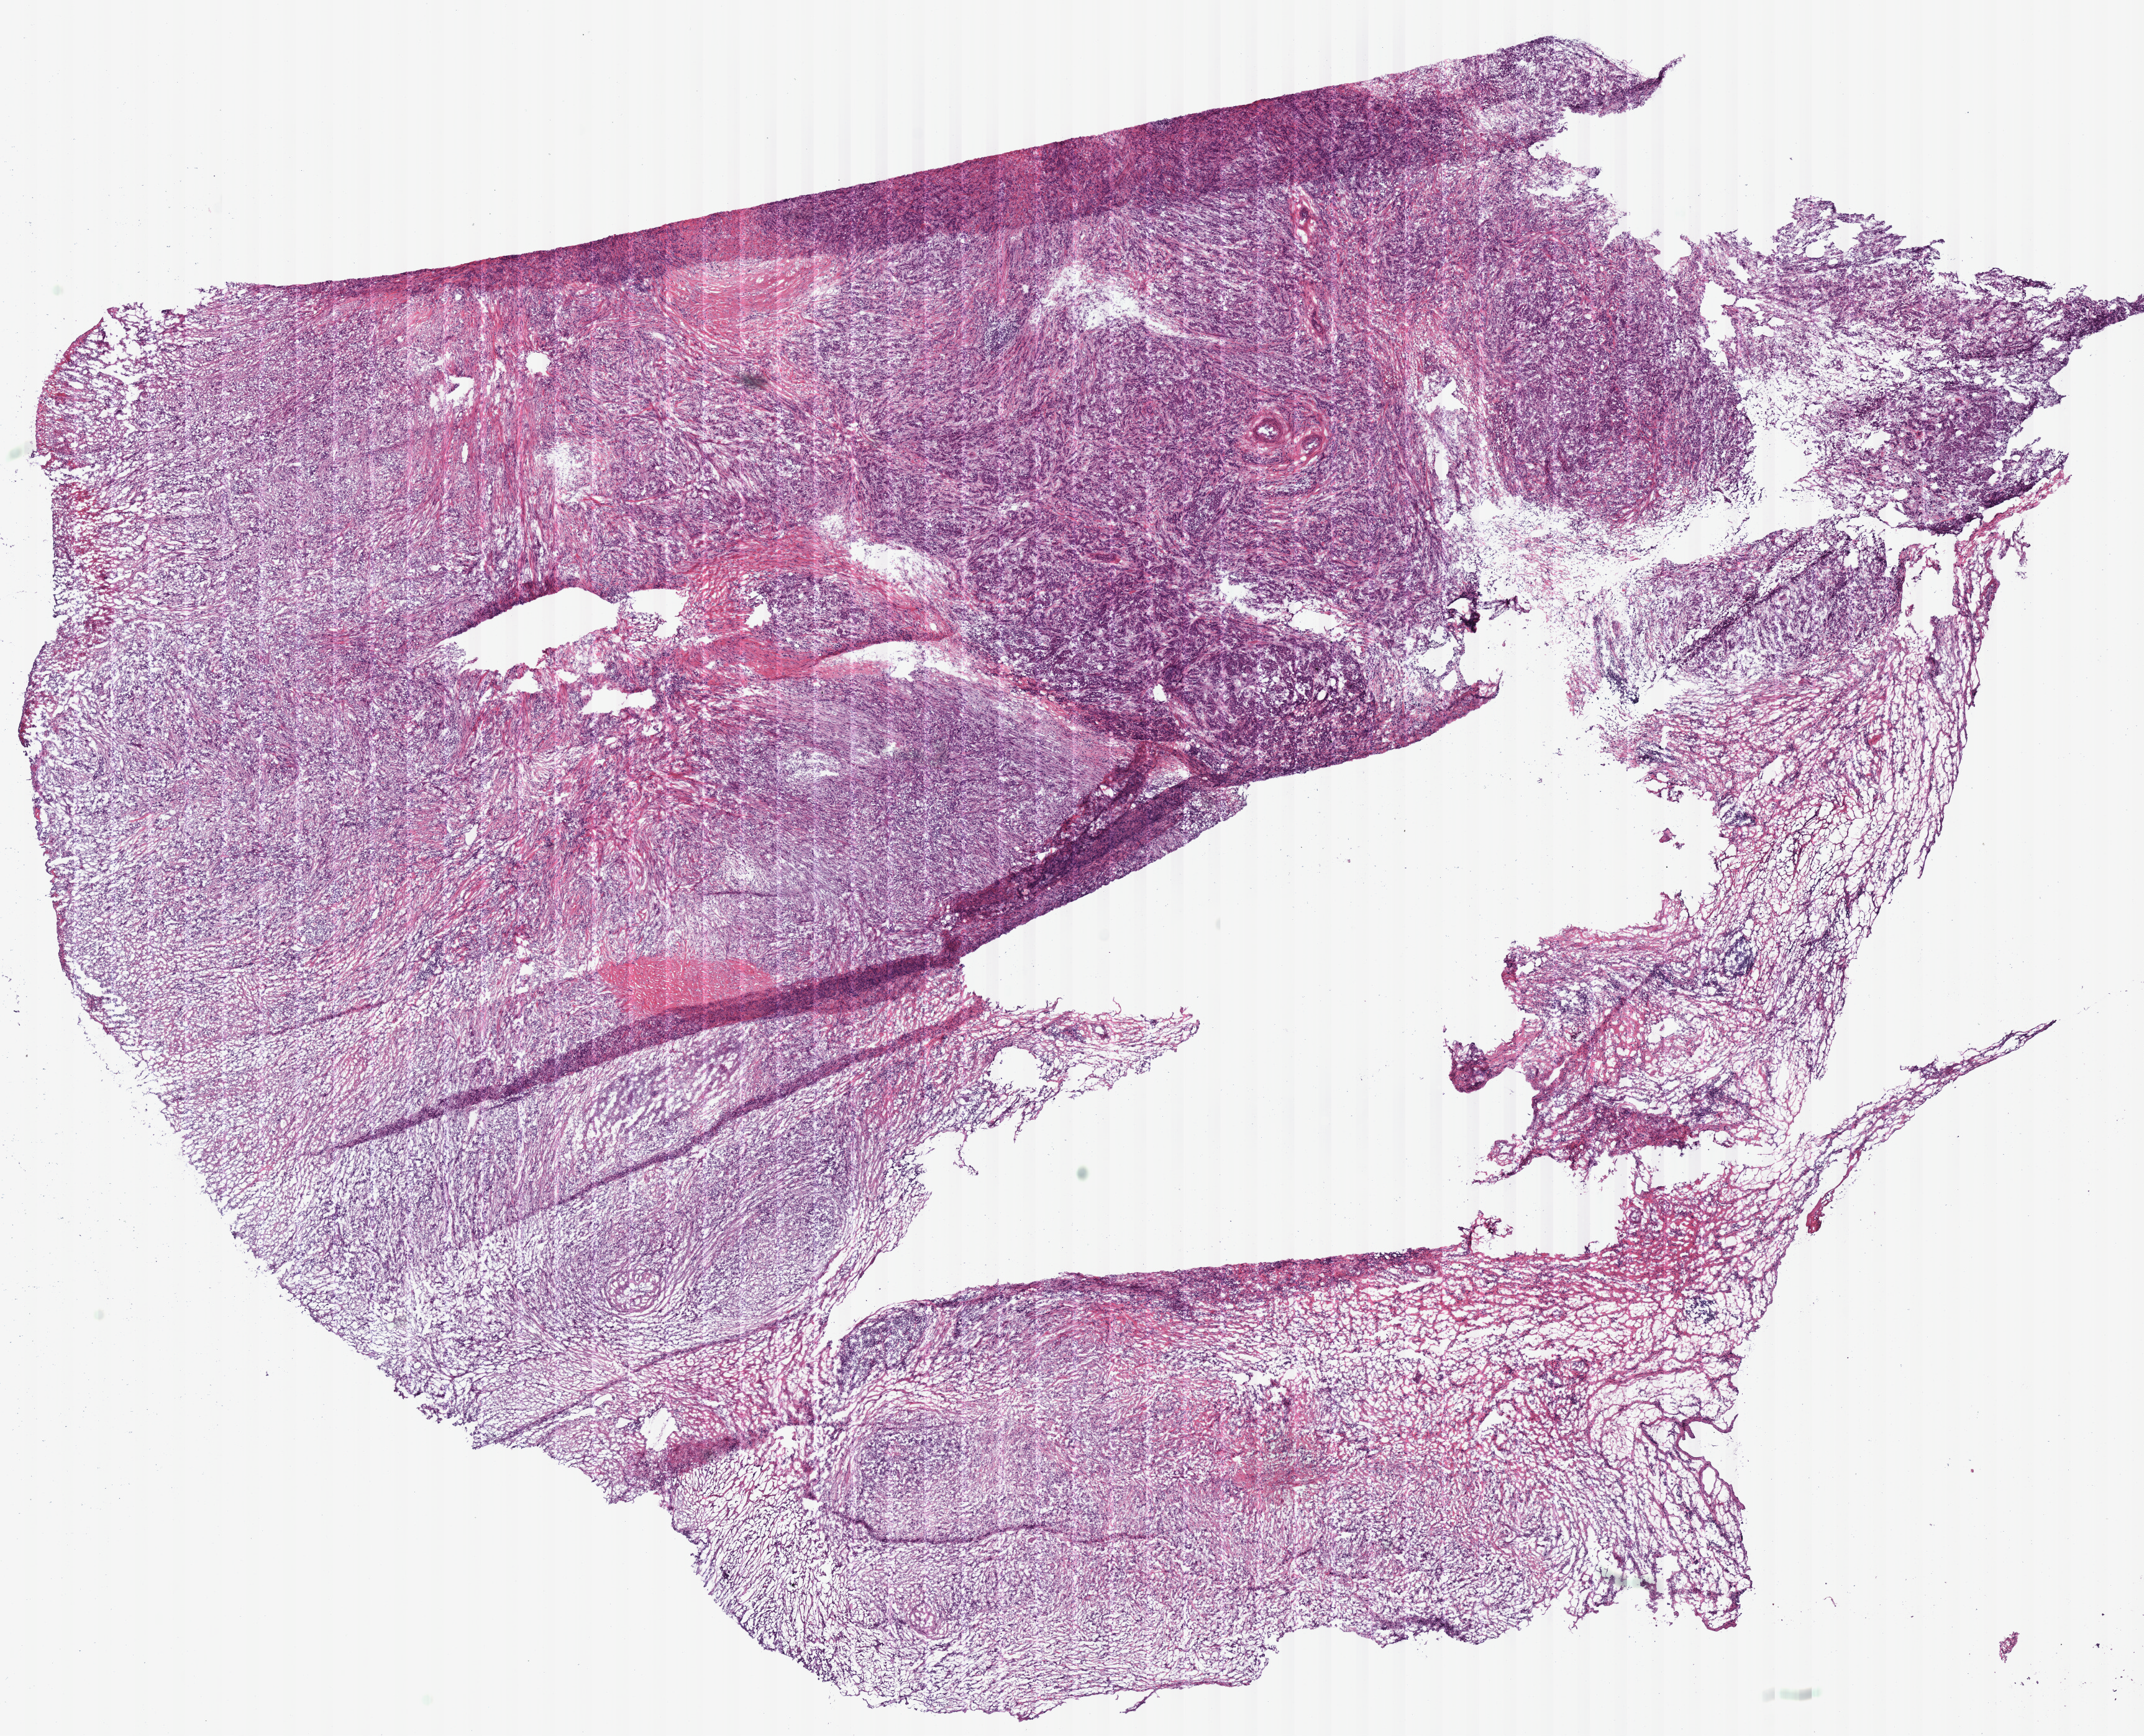
H&E-stained whole-slide image — low-resolution overview of the scanned area, about 13.6 x 11.0 mm. Frozen section from the bottom of the tissue portion. Stomach, primary tumour sample. Patient: female, age at initial diagnosis 80 years. Histologic grade: G3 (poorly differentiated). Slide review estimates, as recorded: tumour cells 82%, tumour nuclei 80%, normal cells 0%, stromal cells 15%, necrosis 3%.
Pathologic diagnosis: Adenocarcinoma, NOS (fundus of stomach). AJCC pathologic stage: IIA (7th edition).